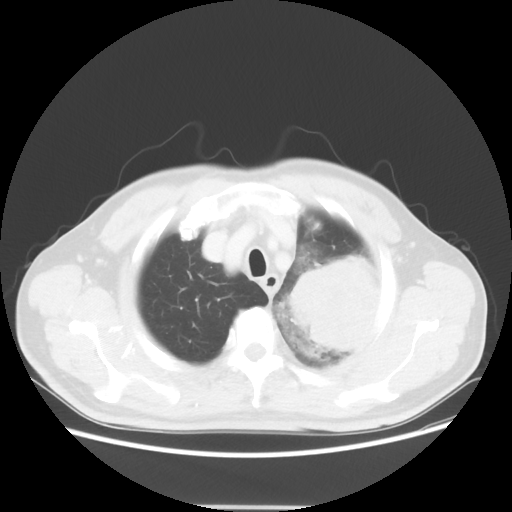
Chest CT, one axial slice; slice 47 of 53 in the series (ordered by position); reconstruction kernel STANDARD; 100 kVp; lung window (W 1500 / L -600 HU); 5 mm slice thickness; 512 × 512 image matrix, field of view 391 × 391 mm. Male patient, age 60 years. Case-level facts recorded for this patient, not image findings: clinical TNM (as recorded): T4 N1 M1a; histopathological grade: G3.
Outlined on this slice (rectangle marked by the reading radiologist):
- lung tumour (recorded histology: large cell carcinoma): bounding box (x1, y1, x2, y2) in pixels: (281, 250, 390, 354)